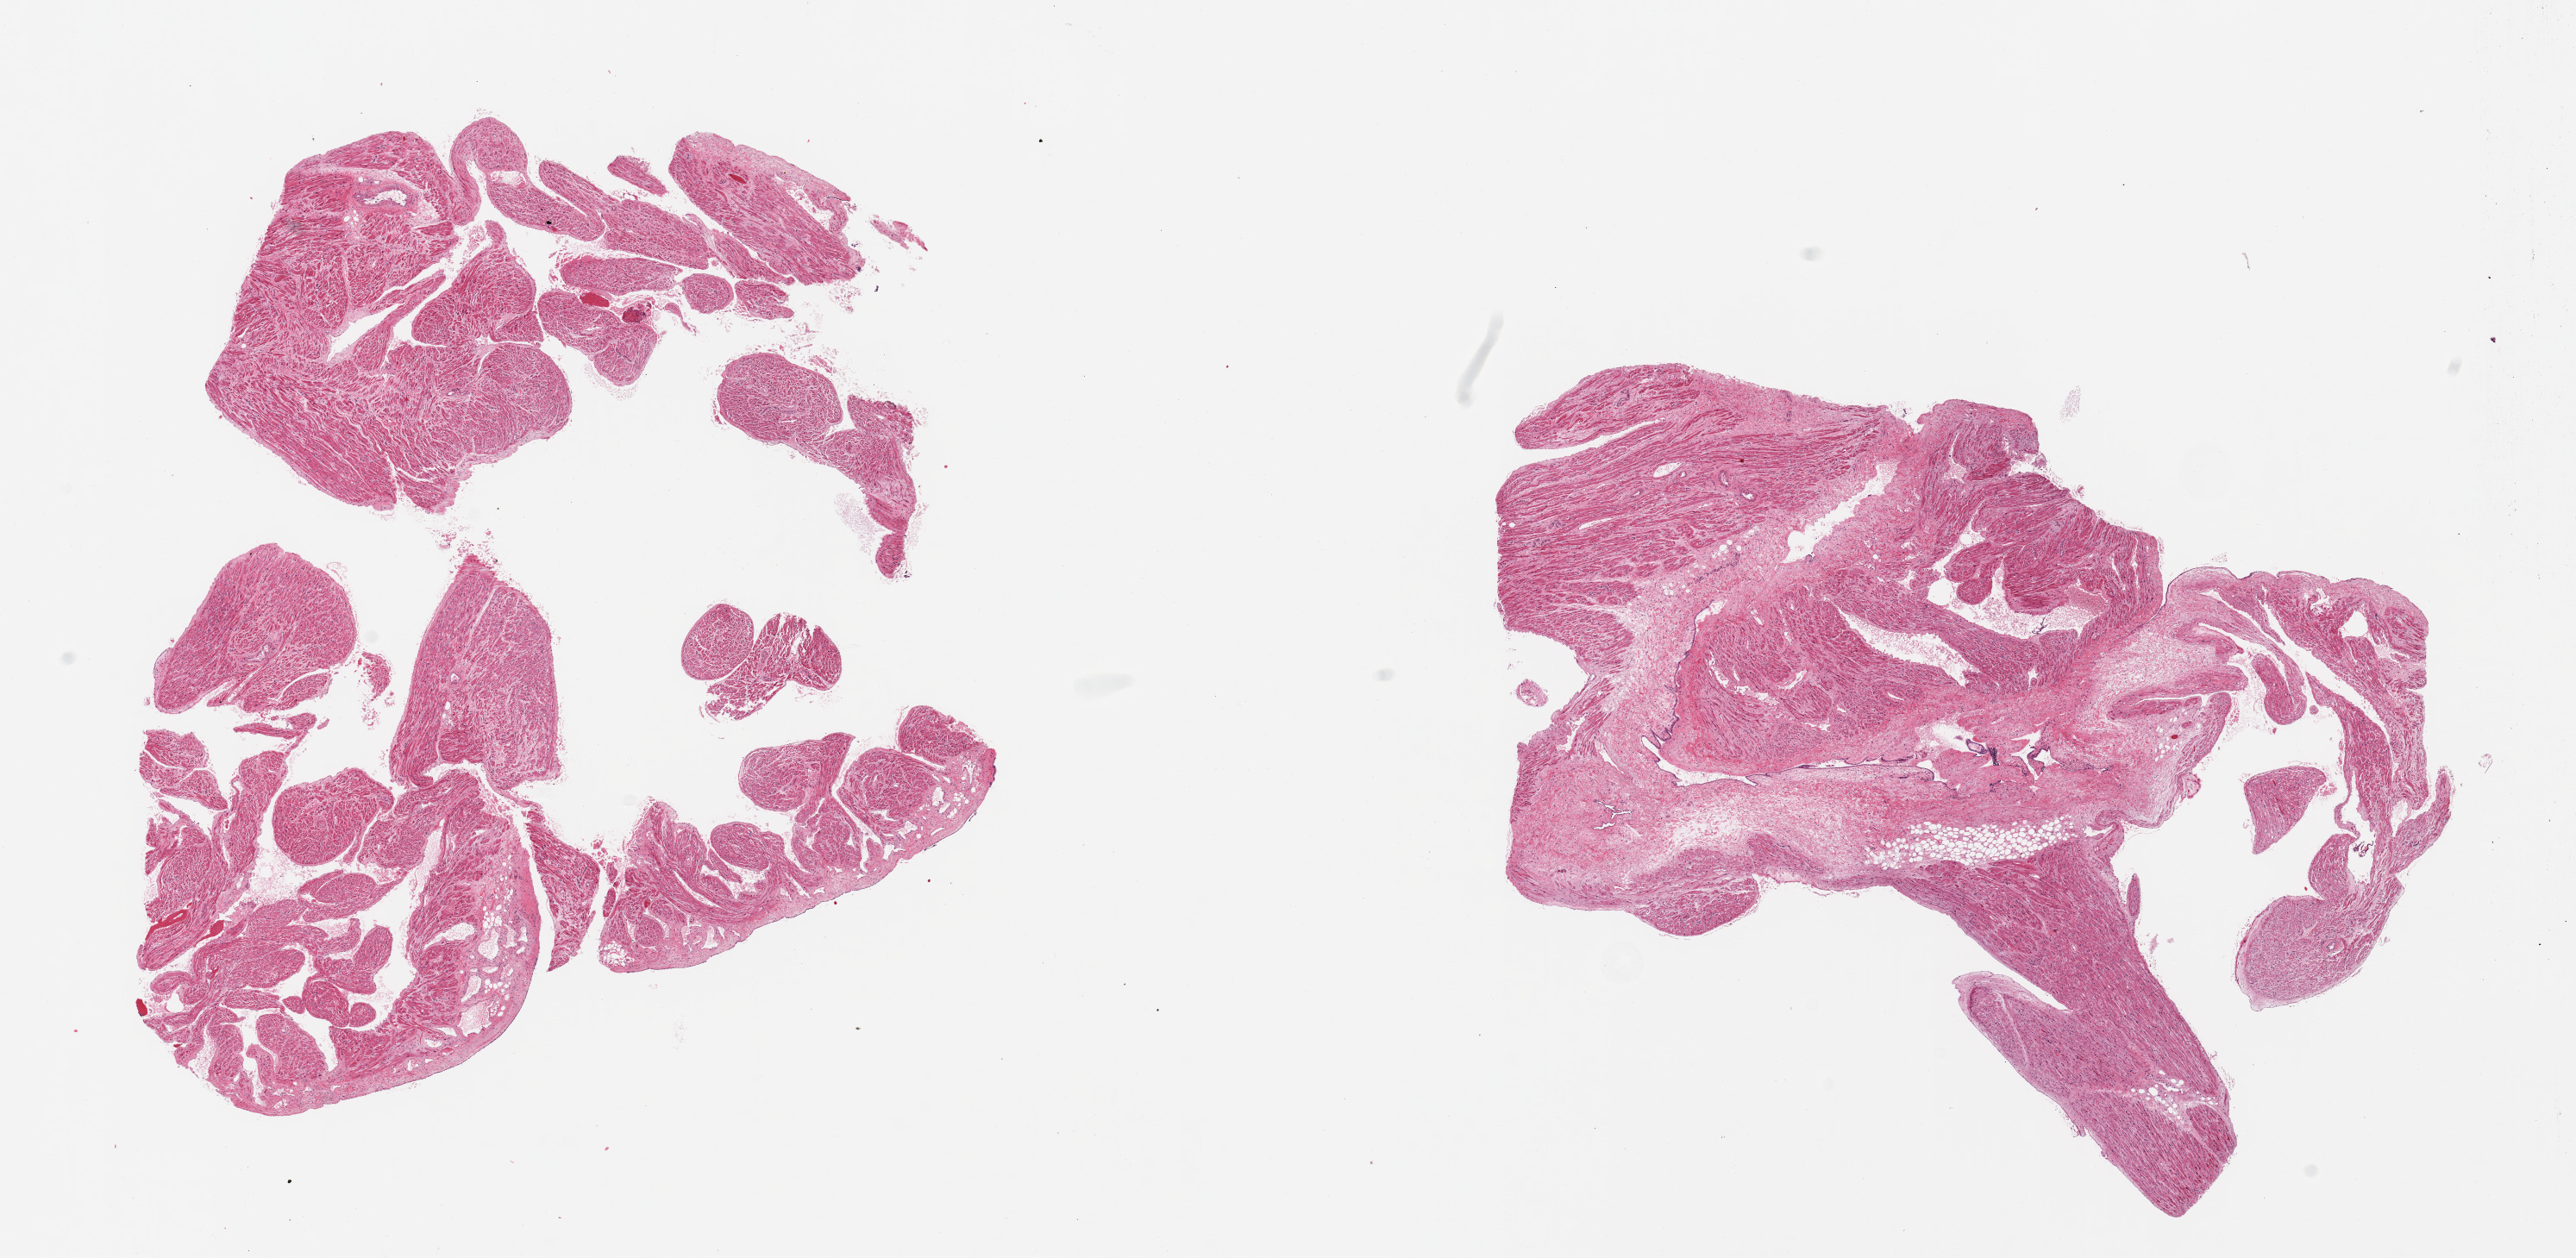
H&E whole-slide image, brightfield, whole scanned area (about 23.6 x 11.5 mm, from a 20x scan) shown as a low-resolution overview. PAXgene-fixed paraffin-embedded (PFPE) section. Sampled site (target tissue): auricular appendage. Tissue donor sample. Donor sex: male.
Pathologist's review note for this sample: 2 pieces, no abnormalities.